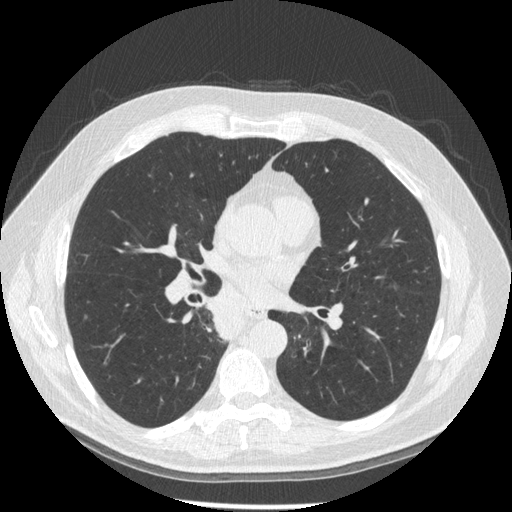
Chest CT (low-dose screening protocol), one axial image, third annual screen, lung window (W 1500 / L -600 HU), 1.25 mm slice thickness, 512 × 512 image matrix, field of view 370 × 370 mm. Male, age 61 years at enrolment. Former smoker at enrolment.
Lesion marked by an expert reader, bounding box <203,298,256,349> (left, top, right, bottom; pixels). Screening reader's record for this exam: no non-calcified nodule ≥4 mm recorded. Official screen result: positive, other. Participant outcome: lung cancer diagnosed 10 days after this screen — squamous cell carcinoma, keratinizing, NOS, right lower lobe, stage IIIB (AJCC 6th edition), 40 mm at pathology.